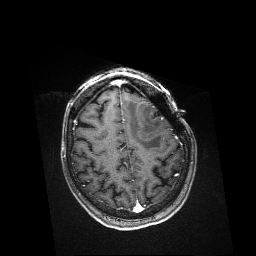
Brain MRI from a brain-tumour surgery series, one axial slice; slice 129 of 176 in the series (ordered by position); T1-weighted post-contrast; 1 mm slice thickness; 256 × 256 image matrix, field of view 256 × 256 mm. Case-level facts recorded for this patient, not image findings: histopathology: Metastatic Melanoma; tumour location: Left Frontal.
Structures marked on this image (manually delineated by an expert):
- residual tumour: bounding box <149,123,155,125> (left, top, right, bottom; pixels)